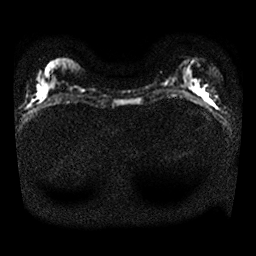
Breast MRI, one axial slice; slice 8 of 25 in the series (ordered by position); diffusion-weighted series; image 2 of 4 stored at this slice position (different b-values; order by instance number); 1.5 T; 4 mm slice thickness; 256 × 256 image matrix, field of view 320 × 320 mm. Female patient.
Structures marked on this image (manually delineated by an expert):
- tumour on diffusion-weighted imaging: box from (x=203, y=93) to (x=210, y=103) px